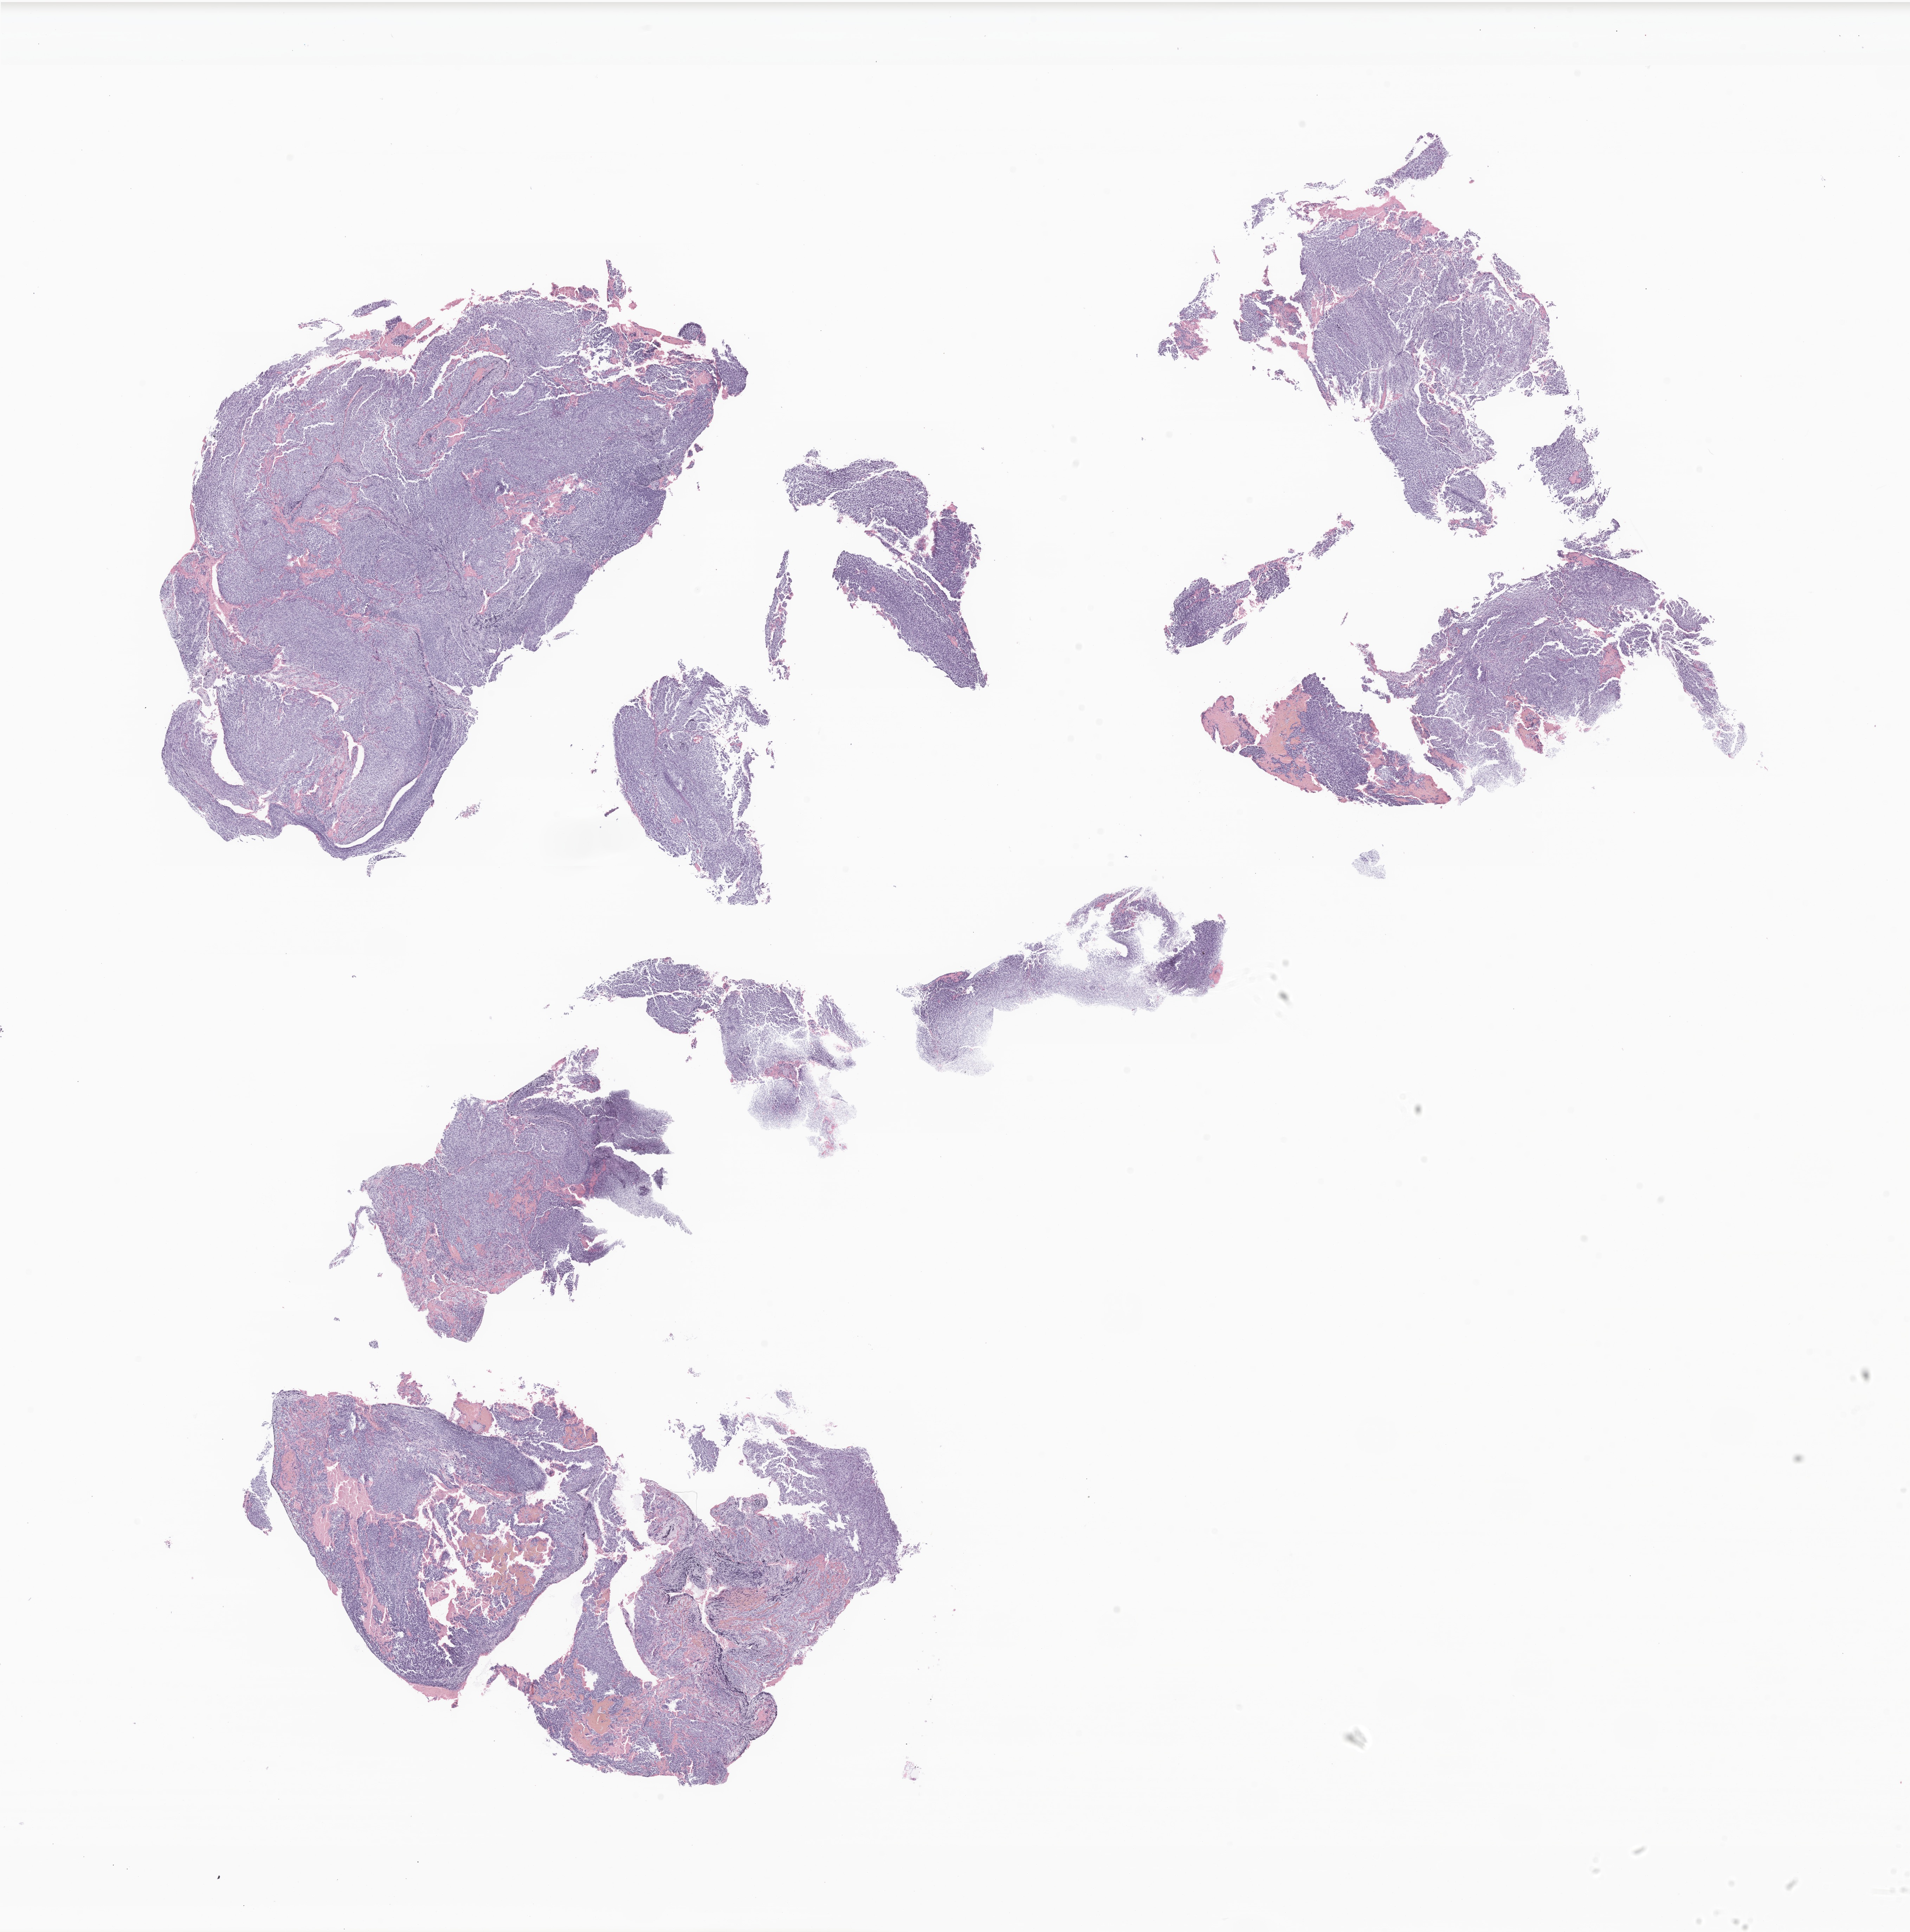
Digitized haematoxylin and eosin-stained section of tumor tissue from the spinal cord, a low-resolution overview of the entire scanned area, about 22.9 x 23.2 mm; formalin-fixed, paraffin-embedded (FFPE) tissue. Patient male; age 145 months (12 years 1 month).
Diagnosis: Glioma, malignant.